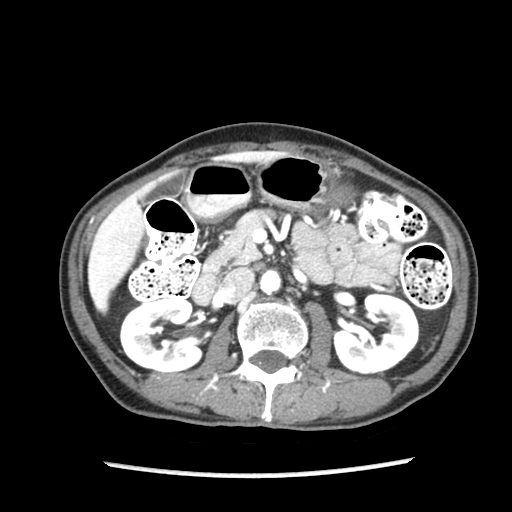
Contrast-enhanced abdominal CT (liver protocol), one axial slice. Slice 40 of 87 in the series (ordered by position). Soft-tissue window (W 400 / L 40 HU). 512 × 512 image matrix, field of view 300 × 300 mm. From the clinical record (not read from this slice): diagnosis: hepatocellular carcinoma (patient treated with transarterial chemoembolisation; whether this scan precedes or follows treatment is not stated here); TNM stage (as recorded): Stage-IIIB; Child-Pugh class: A; tumour differentiation: well differentiated.
Annotated regions visible in this slice (semi-automatic segmentation, software-assisted and operator-edited):
- liver parenchyma outside the tumour (the mass and vessels are separate outlines, so this box may not span the whole liver): box from (x=88, y=192) to (x=143, y=312) px
- liver vessels: (x=91, y=226)–(x=128, y=285)